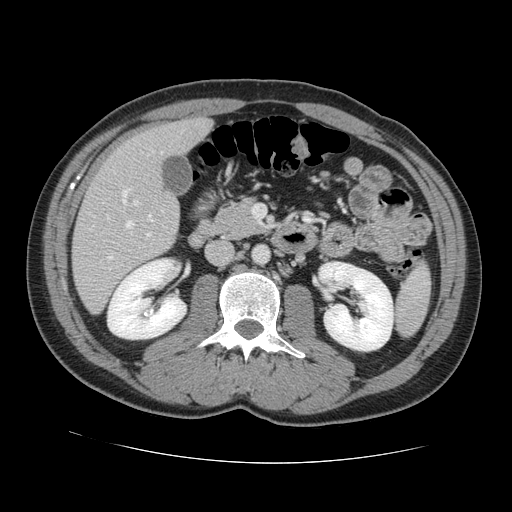
Contrast-enhanced abdominal CT, one axial slice. Slice 55 of 131 in the series (ordered by position). Soft-tissue window (W 400 / L 40 HU). 2.5 mm slice thickness. 512 × 512 image matrix, field of view 380 × 380 mm. Male patient, age 40 years. Case-level facts recorded for this patient, not image findings: diagnosis: colorectal cancer liver metastases, imaged before liver resection; multiple liver metastases: yes; largest metastasis: 2.9 cm; disease in both lobes: yes.
Annotated regions visible in this slice (expert manual segmentation):
- hepatic veins: bounding box [x1, y1, x2, y2] px = [107, 151, 163, 260]
- liver: [73, 118, 211, 311]
- planned liver remnant (the part of the liver to remain after resection): [115, 119, 211, 173]
- portal vein (with intrahepatic branches): [134, 200, 151, 237]